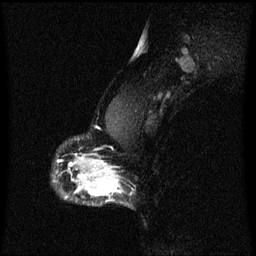
Breast MRI (dynamic contrast-enhanced), one sagittal slice; position 44 of 60 along the scan axis; dynamic contrast-enhanced series, image 2 of 3 at this slice position (ordered by acquisition); 1.5 T; TE 4.2 ms, TR 8.4 ms; 256 × 256 image matrix, field of view 200 × 200 mm. Patient: female, 40 years.
Outlined on this slice (semi-automatically segmented with operator editing):
- analysis volume of interest (the breast-tissue region the enhancement analysis was run in; not a lesion): bounding box (x1, y1, x2, y2) in pixels: (76, 172, 133, 205)
- tumour enhancement mask (voxels above the 70 % enhancement threshold inside the analysis volume of interest): (79, 172, 123, 197)